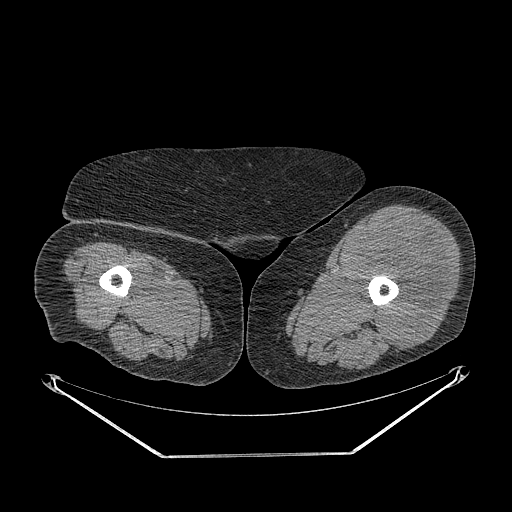
CT of an extremity soft-tissue mass (from a PET/CT study), one axial slice; position 233 of 267 along the scan axis; reconstruction kernel STANDARD; soft-tissue window (W 400 / L 40 HU); 3.75 mm slice thickness; 512 × 512 image matrix. Female patient. From the clinical record (not read from this slice): histological type: undifferentiated – high grade; grade: high; site of the primary tumour: left thigh.
Annotated regions visible in this slice (expert contour drawn on MRI and transferred to this co-registered scan by the dataset authors):
- gross tumour volume including surrounding oedema: bounding box [x1, y1, x2, y2] px = [354, 215, 451, 348]
- gross tumour volume (mass): [354, 215, 449, 348]